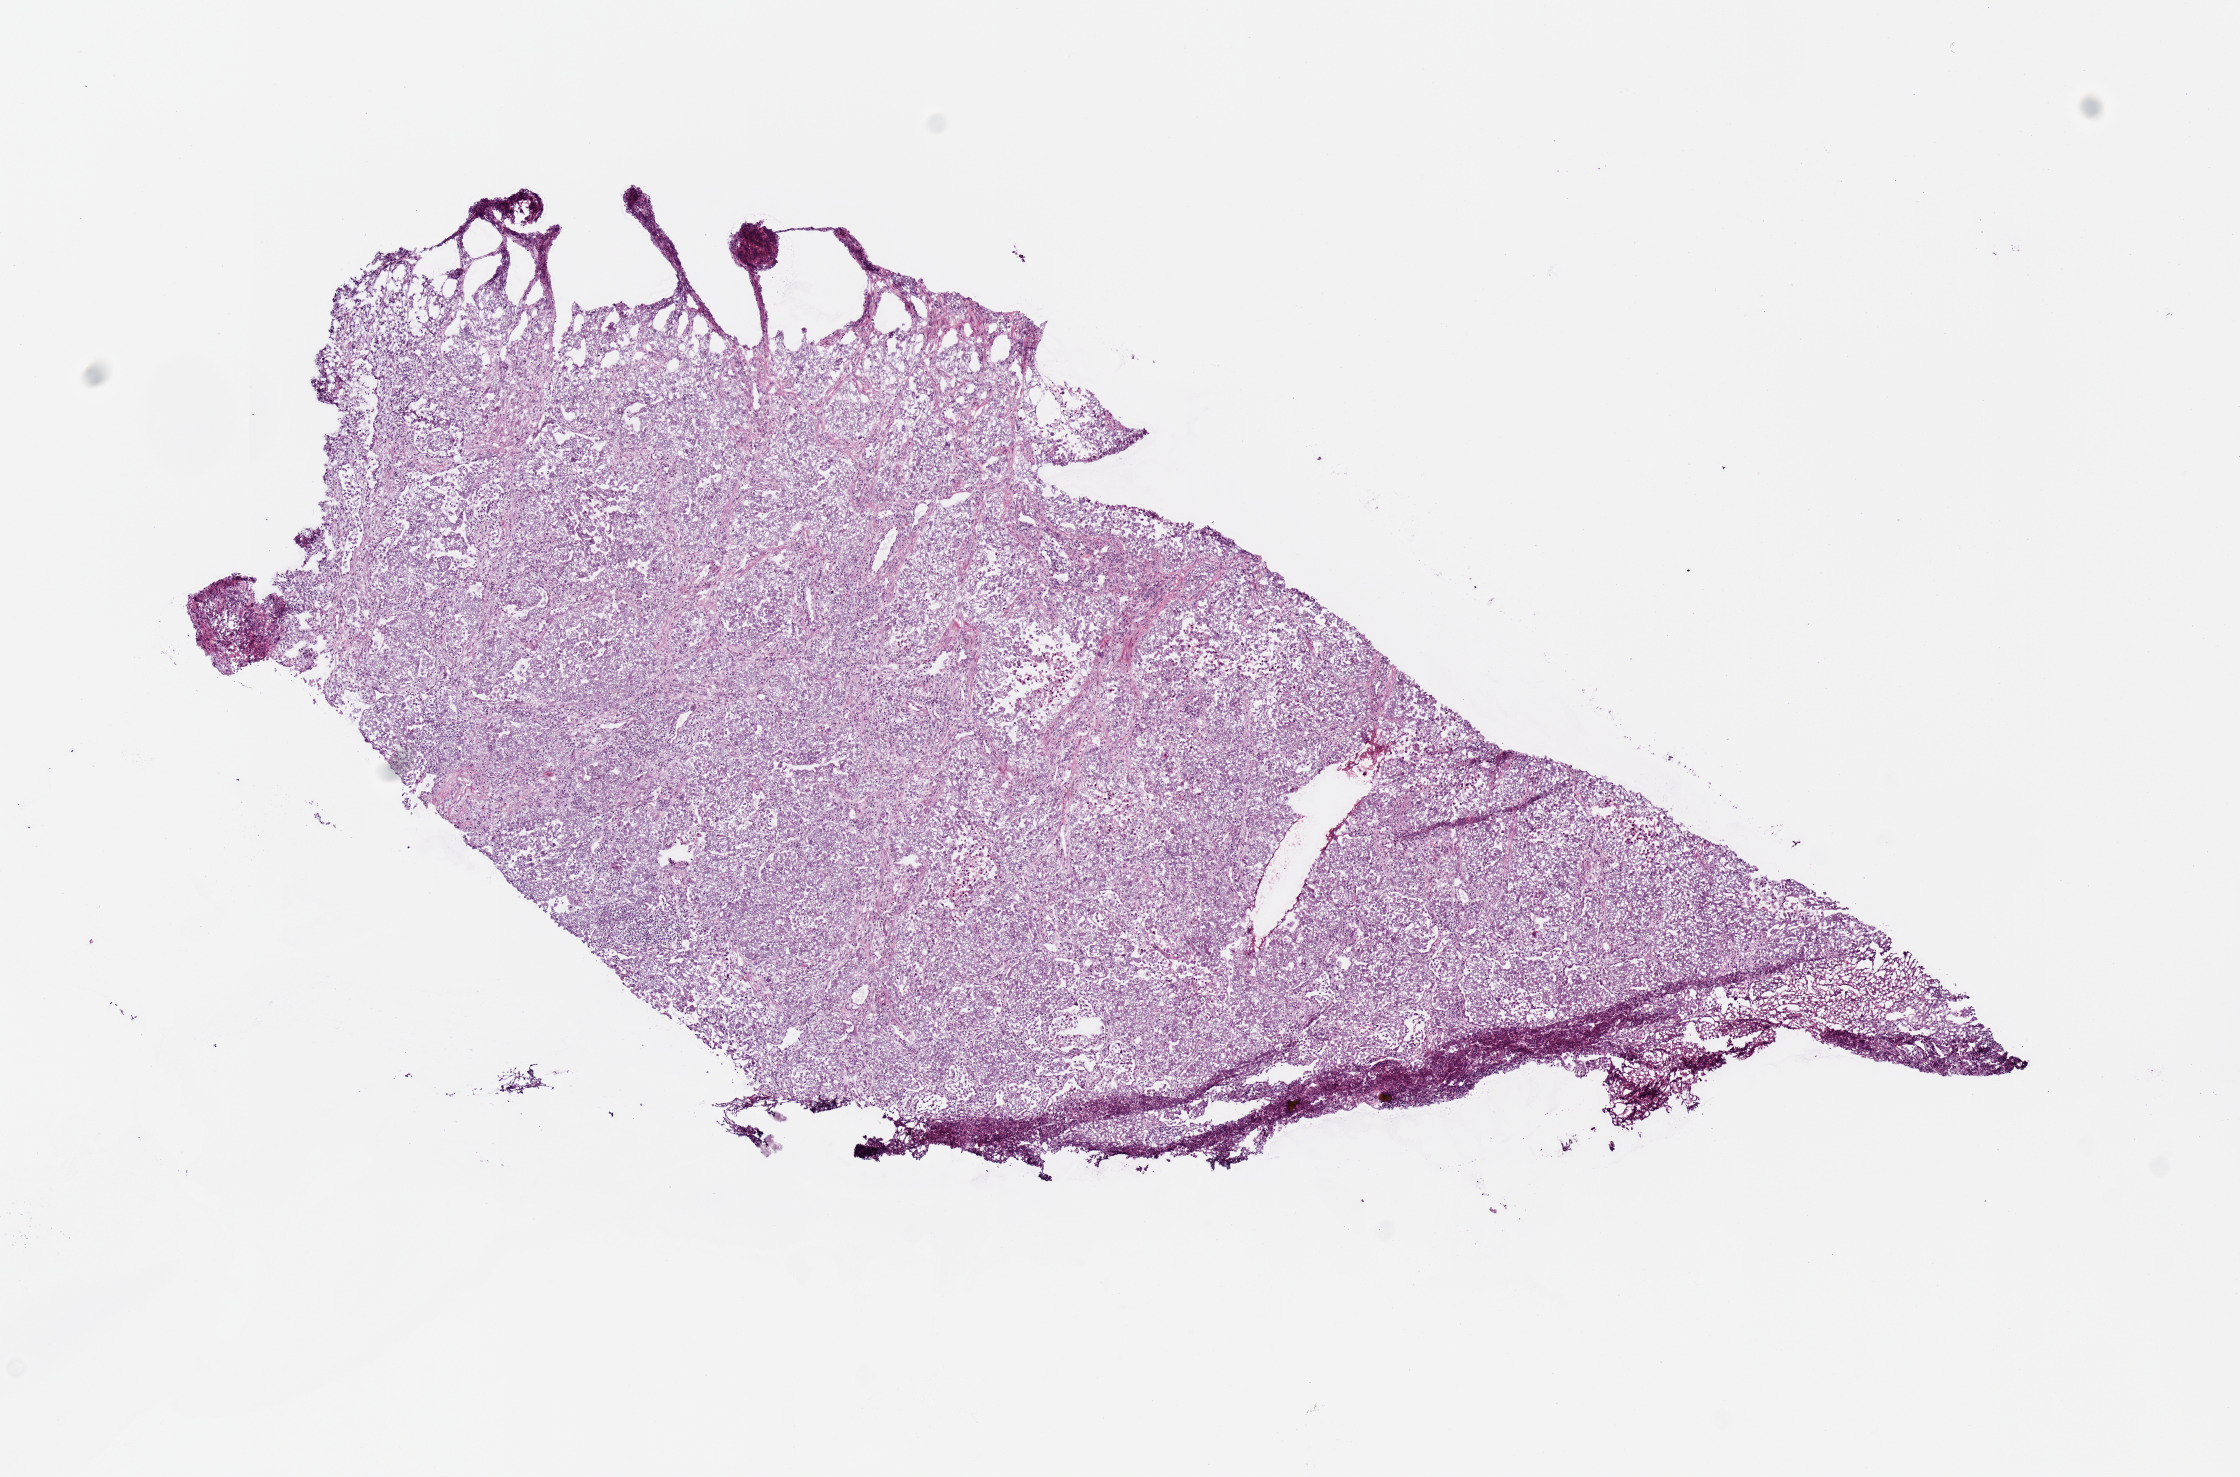
H&E whole-slide image — a low-resolution overview of the entire scanned area, about 8.9 x 5.8 mm; frozen section; lung, primary tumour sample. Male patient; age at initial diagnosis 81 years. Slide review estimates, as recorded: tumour cells 99%, tumour nuclei 70%, normal cells 0%, stromal cells 0%, necrosis 1%. Inflammatory infiltration, as recorded: lymphocyte infiltration 20%, monocyte infiltration 1%, neutrophil infiltration 1%.
AJCC pathologic stage: IIA (7th edition). TNM: T2b N0 MX. Histologic diagnosis: Adenocarcinoma, NOS (middle lobe, lung).